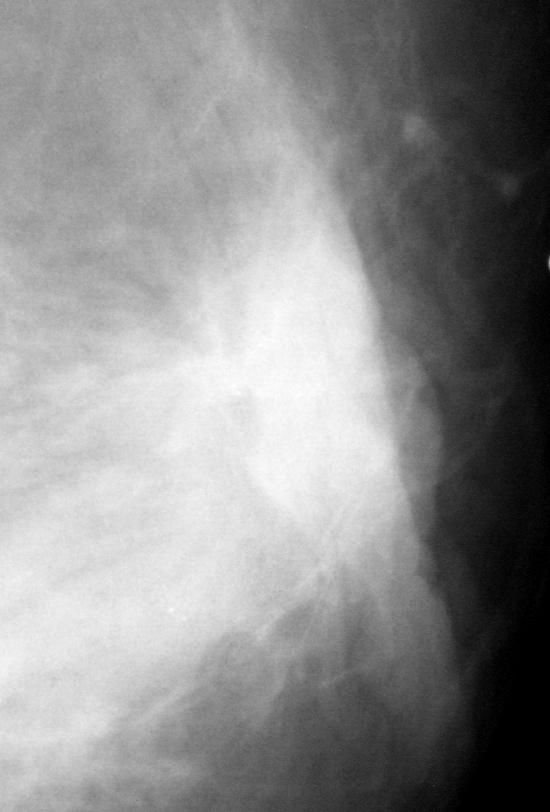
Region of interest cut from a scanned film mammogram (one marked finding); left breast; MLO view; BI-RADS breast density category 2 (scale 1–4).
Marked abnormality: mass, shape irregular, margins spiculated; BI-RADS assessment category 5; pathology result (as recorded, not read from the image): malignant.